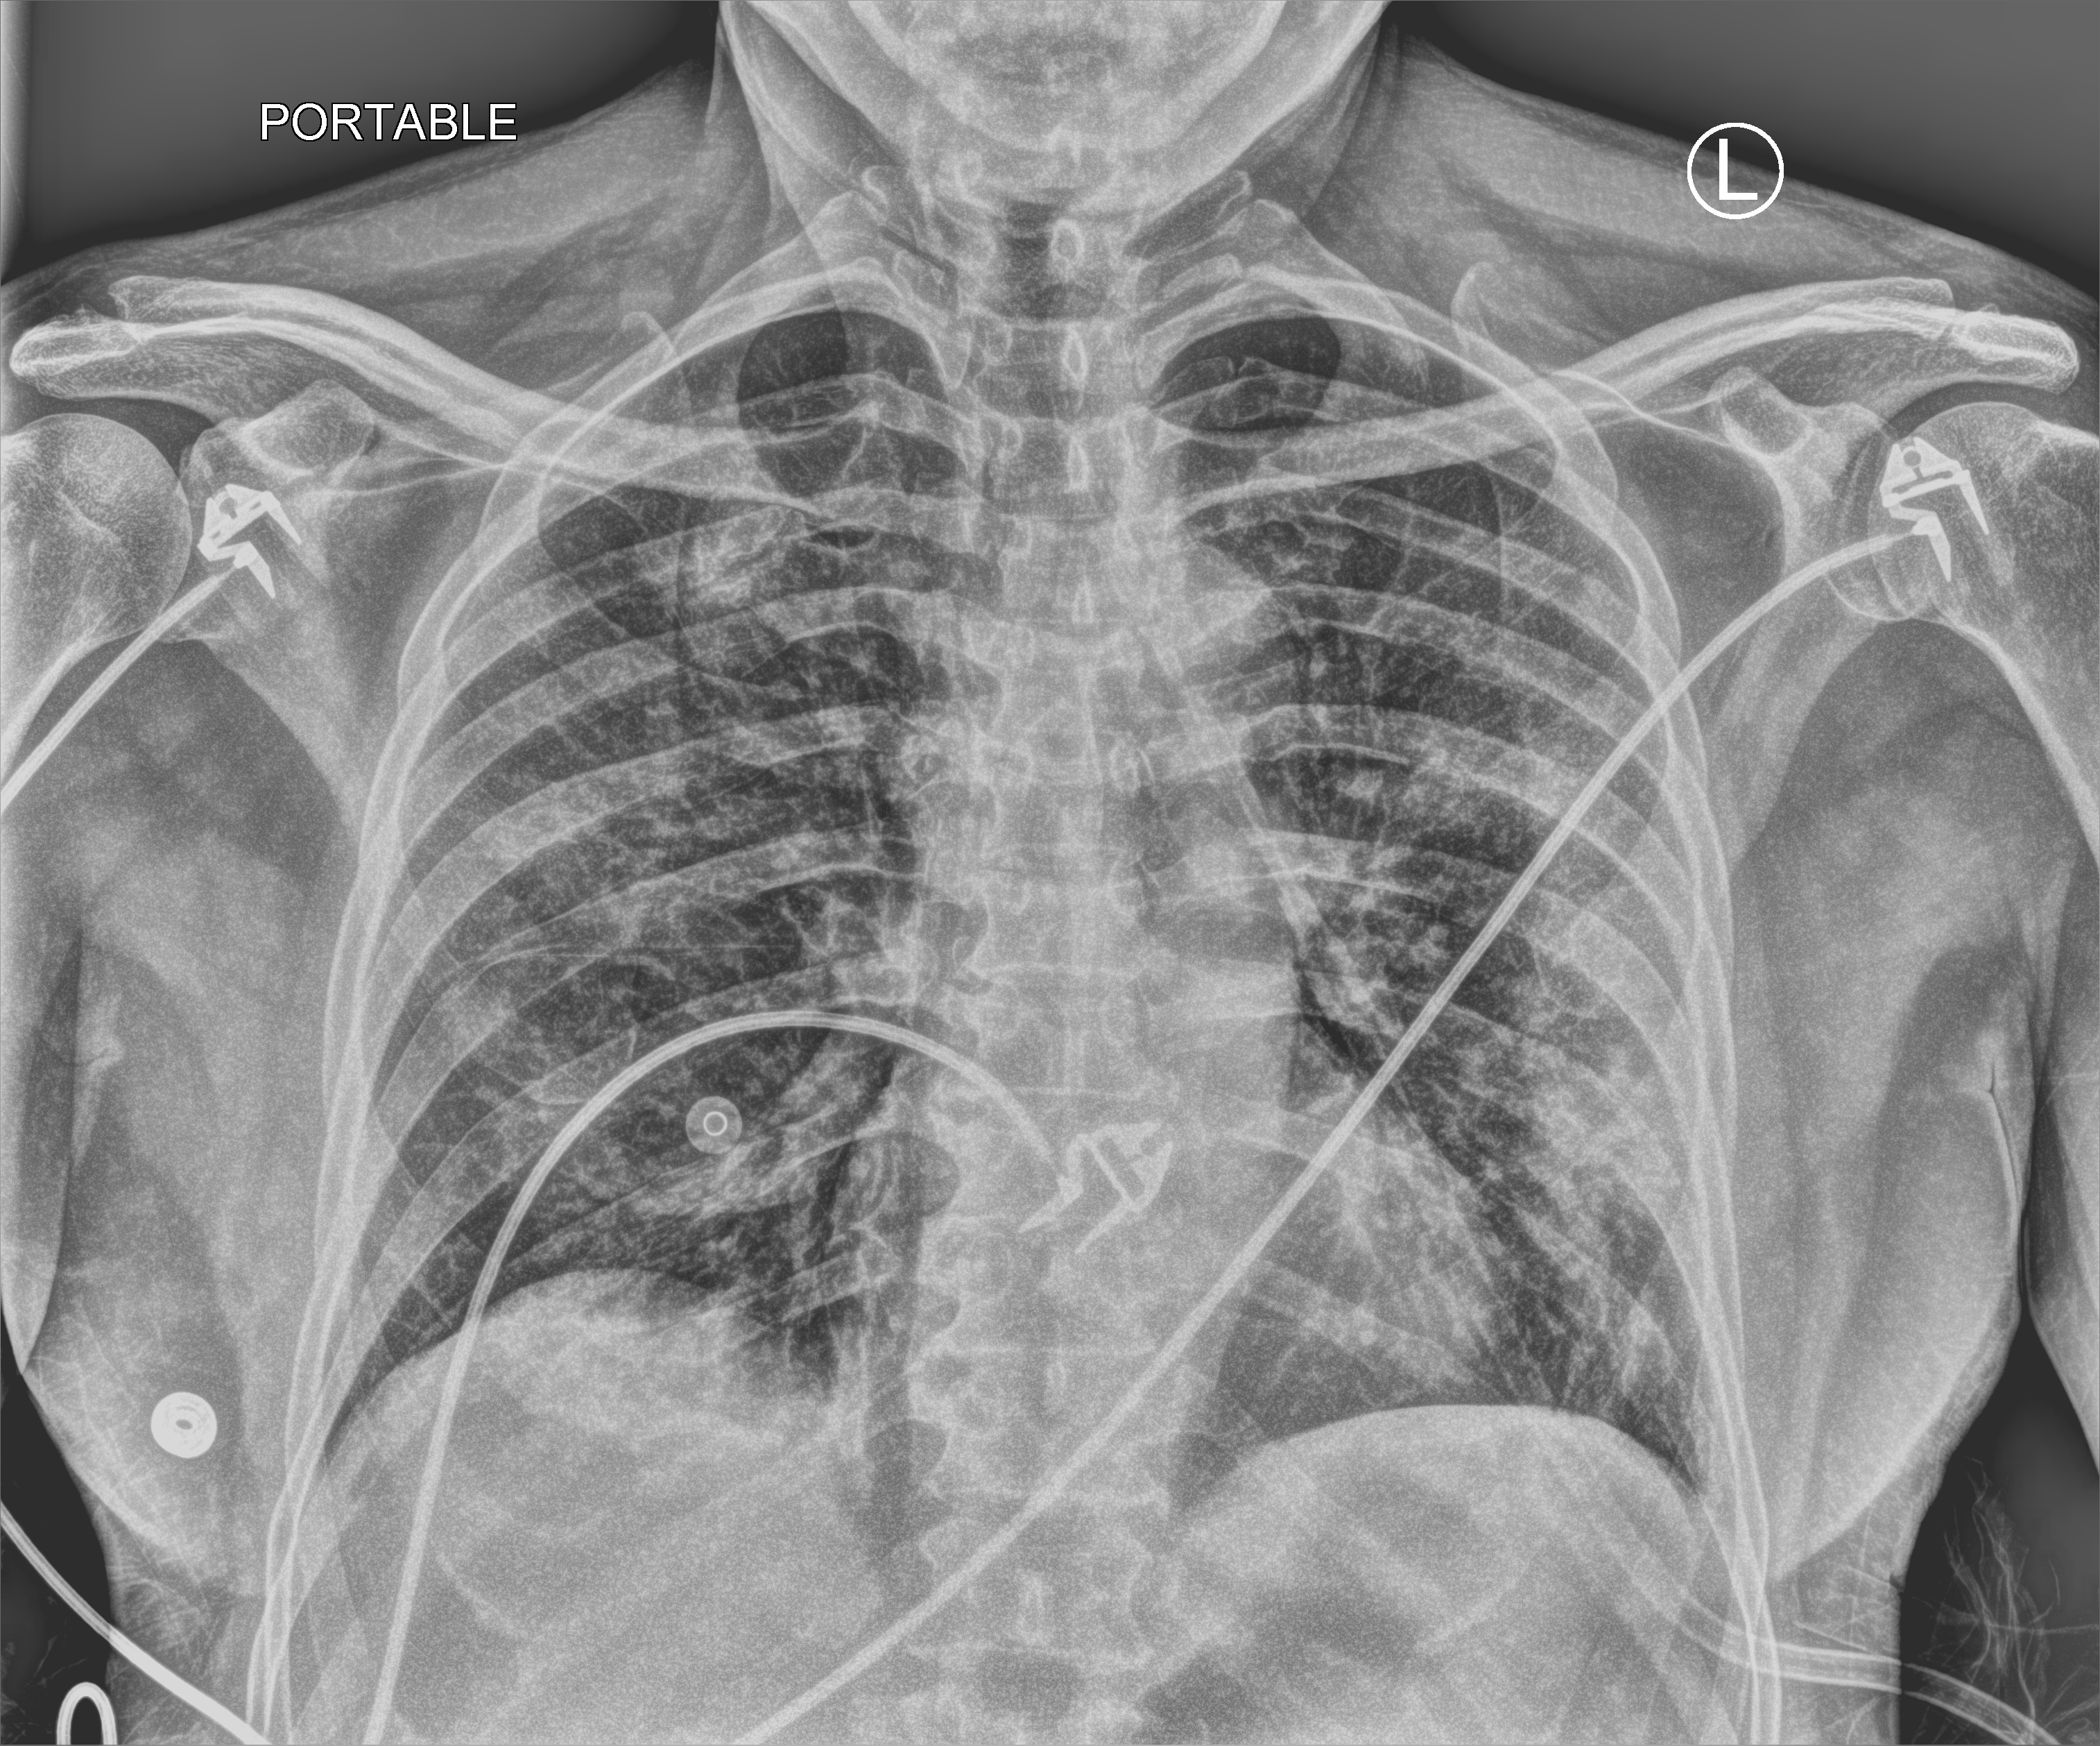
Bedside chest radiograph (computed radiography), anteroposterior (AP) projection. Male patient hospitalised with COVID-19, age 60–74 years.
From the hospital-stay record, not from the radiograph (when in the stay this image was taken is not recorded): hypertension (admission record): yes; other chronic lung disease (admission record): no.